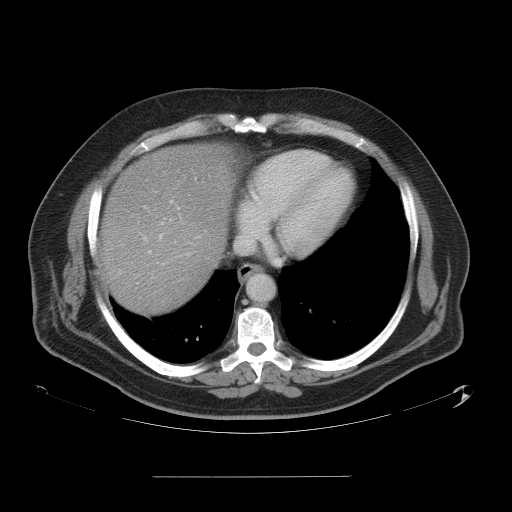
Contrast-enhanced abdominal CT, one axial slice; position 50 of 58 along the scan axis; intravenous contrast given; soft-tissue window (W 400 / L 40 HU); 5 mm slice thickness; 512 × 512 image matrix, field of view 480 × 480 mm. Male patient, age 63 years. From the clinical record (not read from this slice): diagnosis: colorectal cancer liver metastases, imaged before liver resection; multiple liver metastases: no; largest metastasis: 4.2 cm; chemotherapy before resection: yes.
Annotated regions visible in this slice (expert manual segmentation):
- hepatic veins: box from (x=158, y=205) to (x=246, y=261) px
- liver: (x=102, y=144)–(x=234, y=314)
- planned liver remnant (the part of the liver to remain after resection): (x=102, y=210)–(x=220, y=314)
- portal vein (with intrahepatic branches): (x=149, y=178)–(x=196, y=254)